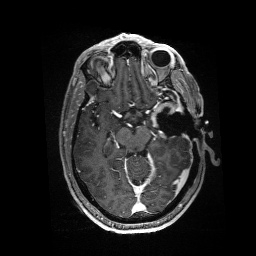
Brain MRI from a brain-tumour surgery series, one axial slice. Position 98 of 176 along the scan axis. T1-weighted post-contrast. 1 mm slice thickness. 256 × 256 image matrix. Case-level facts recorded for this patient, not image findings: histopathology: Glioblastoma; WHO grade: 4; IDH mutation: no; tumour location: Left Anterior/Superior Temporal.
Structures marked on this image (outlined manually by an expert reader):
- residual tumour: box from (x=151, y=102) to (x=184, y=127) px